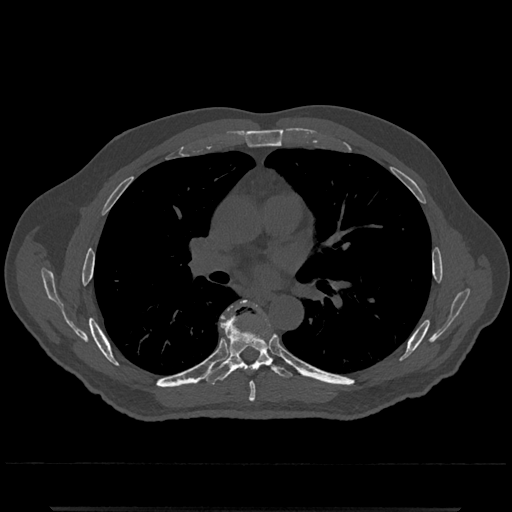
CT including the spine, one axial slice; position 741 of 797 along the scan axis; 120 kVp; bone window (W 1800 / L 400 HU); 0.5 mm slice thickness; 512 × 512 image matrix, field of view 393 × 393 mm. Patient: male, 67 years. From the clinical record (not read from this slice): primary cancer: prostate.
Annotated regions visible in this slice (semi-automatically segmented with operator editing):
- T6 vertebra: bounding box [x1, y1, x2, y2] px = [249, 383, 256, 402]
- T7 vertebra: [203, 302, 293, 385]